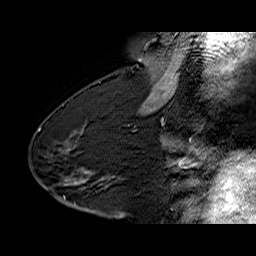
Breast MRI (dynamic contrast-enhanced), one sagittal slice; slice 36 of 60 in the series (ordered by position); dynamic contrast-enhanced series, time point 2 of 6 at this slice position (early post-contrast); 1.5 T; TE 6.4 ms, TR 32.9 ms; 256 × 256 image matrix. Female patient. From the clinical record (not read from this slice): setting: breast cancer imaged before/during neoadjuvant chemotherapy; receptor status: HR-positive, HER2-negative.
Annotated regions visible in this slice (semi-automatically segmented with operator editing):
- analysis volume of interest (the breast-tissue region the enhancement analysis was run in; not a lesion): bounding box [x1, y1, x2, y2] px = [68, 154, 122, 203]
- tumour enhancement mask (voxels above the 100 % enhancement threshold inside the analysis volume of interest): [81, 181, 84, 183]